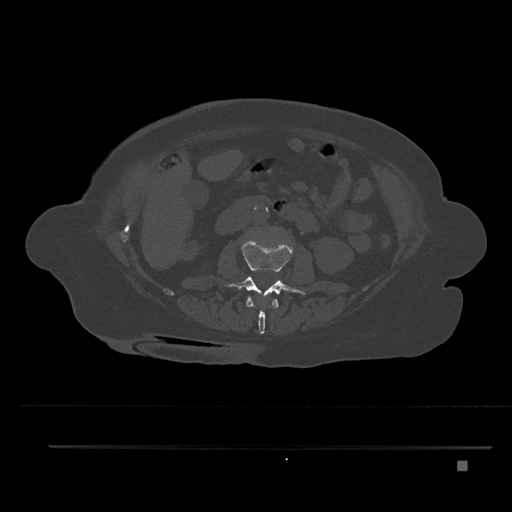
CT including the spine, one axial slice. Slice 175 of 797 in the series (ordered by position). 120 kVp. Bone window (W 1800 / L 400 HU). 0.5 mm slice thickness. 512 × 512 image matrix, field of view 437 × 437 mm. Female patient, age 76 years. Case-level facts recorded for this patient, not image findings: primary cancer: lung; vertebrae with lytic lesions (as recorded): T11, L3.
Annotated regions visible in this slice (semi-automatically segmented with operator editing):
- L1 vertebra: bounding box (x1, y1, x2, y2) in pixels: (246, 296, 279, 334)
- L2 vertebra: (223, 239, 306, 303)